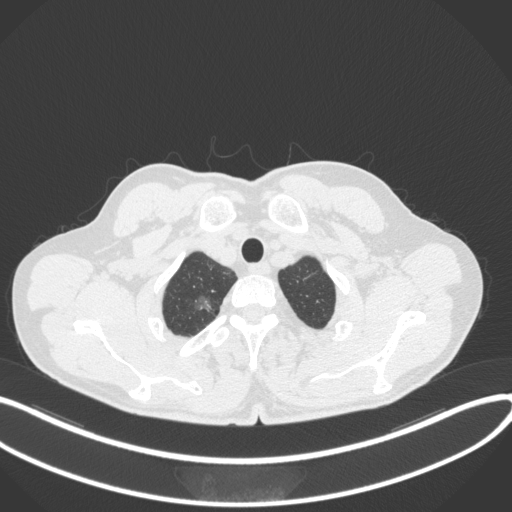
Chest CT, one axial slice. Slice 352 of 407 in the series (ordered by position). Reconstruction kernel B31f. 120 kVp. Lung window (W 1500 / L -600 HU). 1 mm slice thickness. 512 × 512 image matrix, field of view 400 × 400 mm. Patient: male, 58 years. Case-level facts recorded for this patient, not image findings: clinical TNM (as recorded): T1c N0 M0; histopathological grade: G1-2.
Structures marked on this image (bounding box drawn by a radiologist):
- lung tumour (recorded histology: adenocarcinoma): bounding box <183,289,219,321> (left, top, right, bottom; pixels)